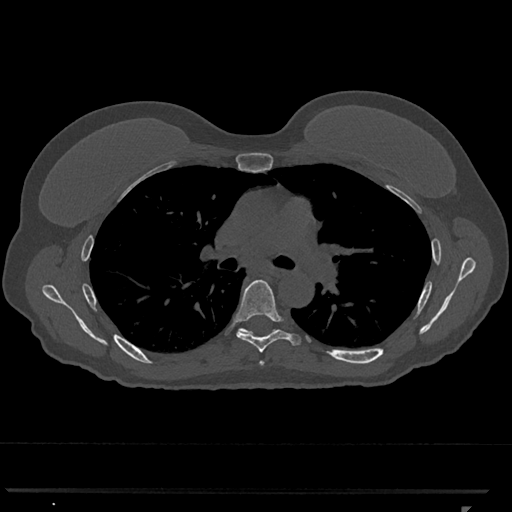
CT including the spine, one axial slice; slice 757 of 793 in the series (ordered by position); reconstruction kernel Br40s/3; 120 kVp; bone window (W 1800 / L 400 HU); 0.5 mm slice thickness; 512 × 512 image matrix, field of view 380 × 380 mm. Patient: female, 62 years. From the clinical record (not read from this slice): primary cancer: renal.
Structures marked on this image (semi-automatically segmented with operator editing):
- T5 vertebra: box from (x=259, y=360) to (x=264, y=365) px
- T6 vertebra: (x=235, y=279)–(x=301, y=353)
- T7 vertebra: (x=242, y=328)–(x=246, y=331)